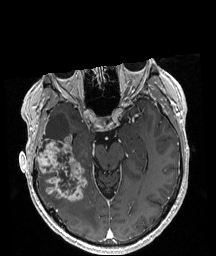
Brain MRI from a brain-tumour surgery series, one axial slice. Slice 123 of 208 in the series (ordered by position). T1-weighted post-contrast. 1 mm slice thickness. 216 × 256 image matrix, field of view 211 × 250 mm. Case-level facts recorded for this patient, not image findings: histopathology: Astrocytoma; WHO grade: 4; IDH mutation: yes.
Outlined on this slice (expert manual segmentation):
- tumour: bounding box <35,134,88,202> (left, top, right, bottom; pixels)